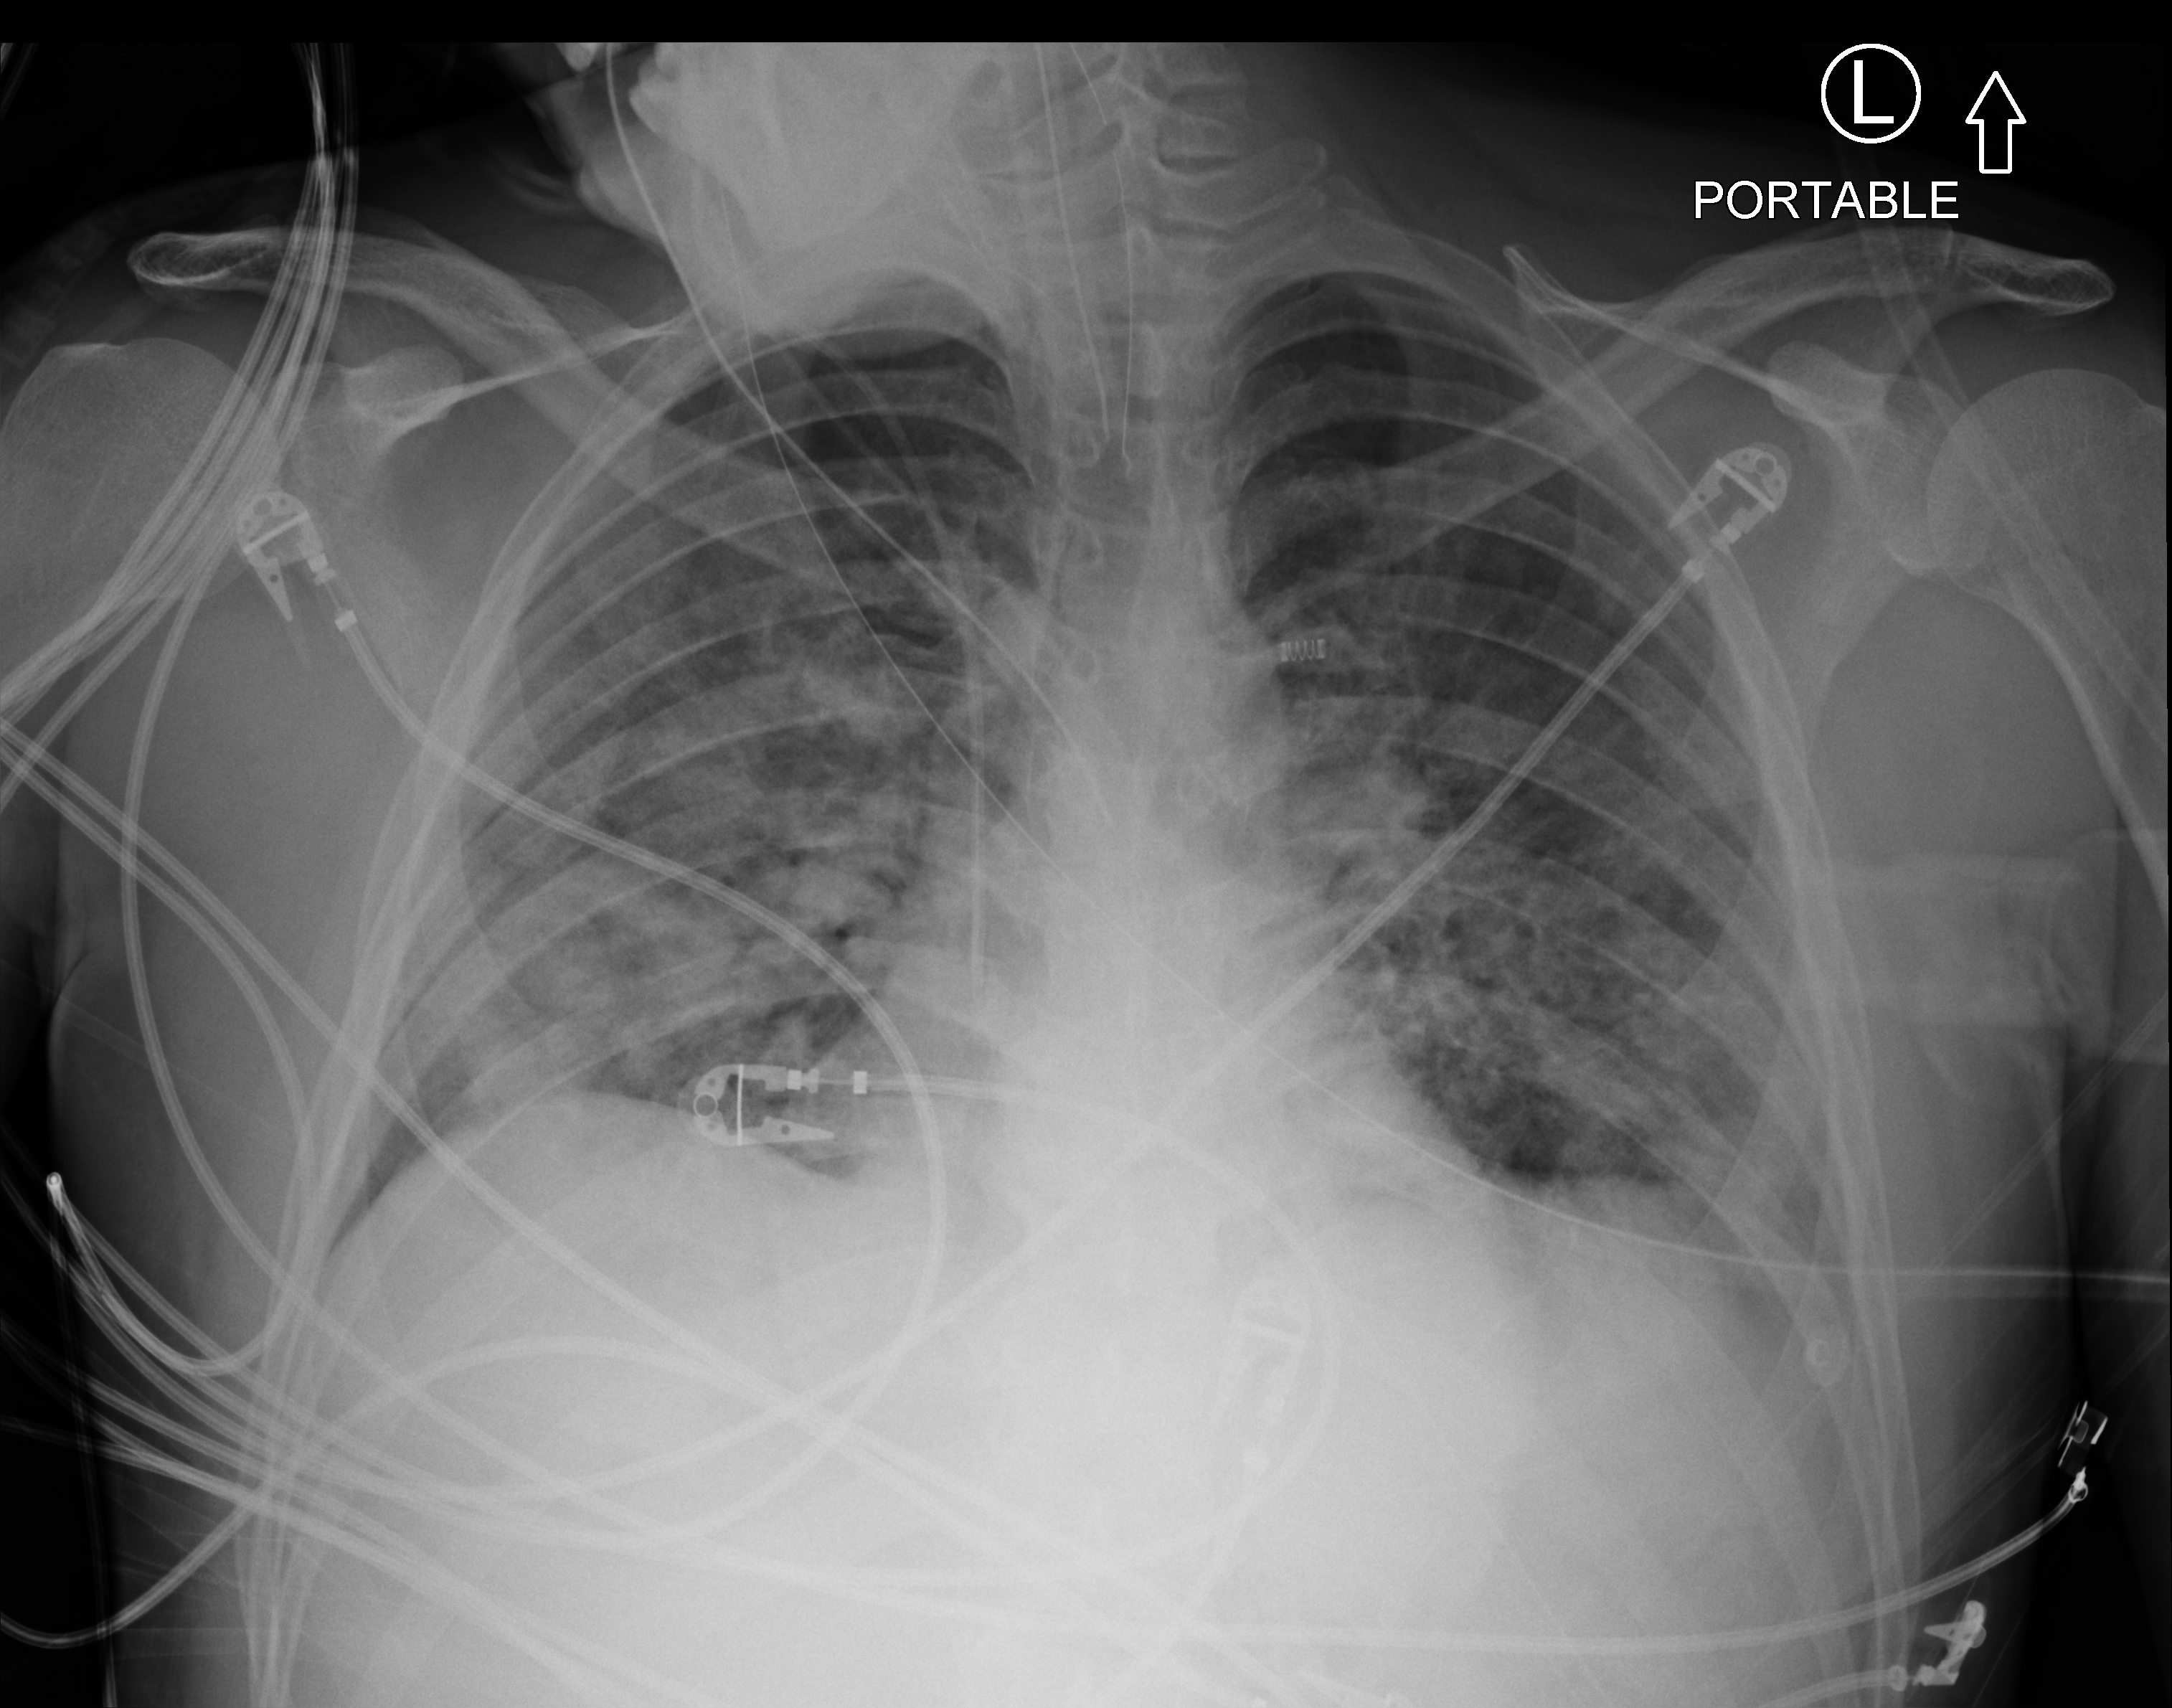
Portable chest radiograph, anteroposterior (AP) projection. Male patient hospitalised with COVID-19, age 18–59 years.
Hospital-stay facts (about this admission, not read from this image; timing relative to this image not recorded): length of hospital stay: 29 days.